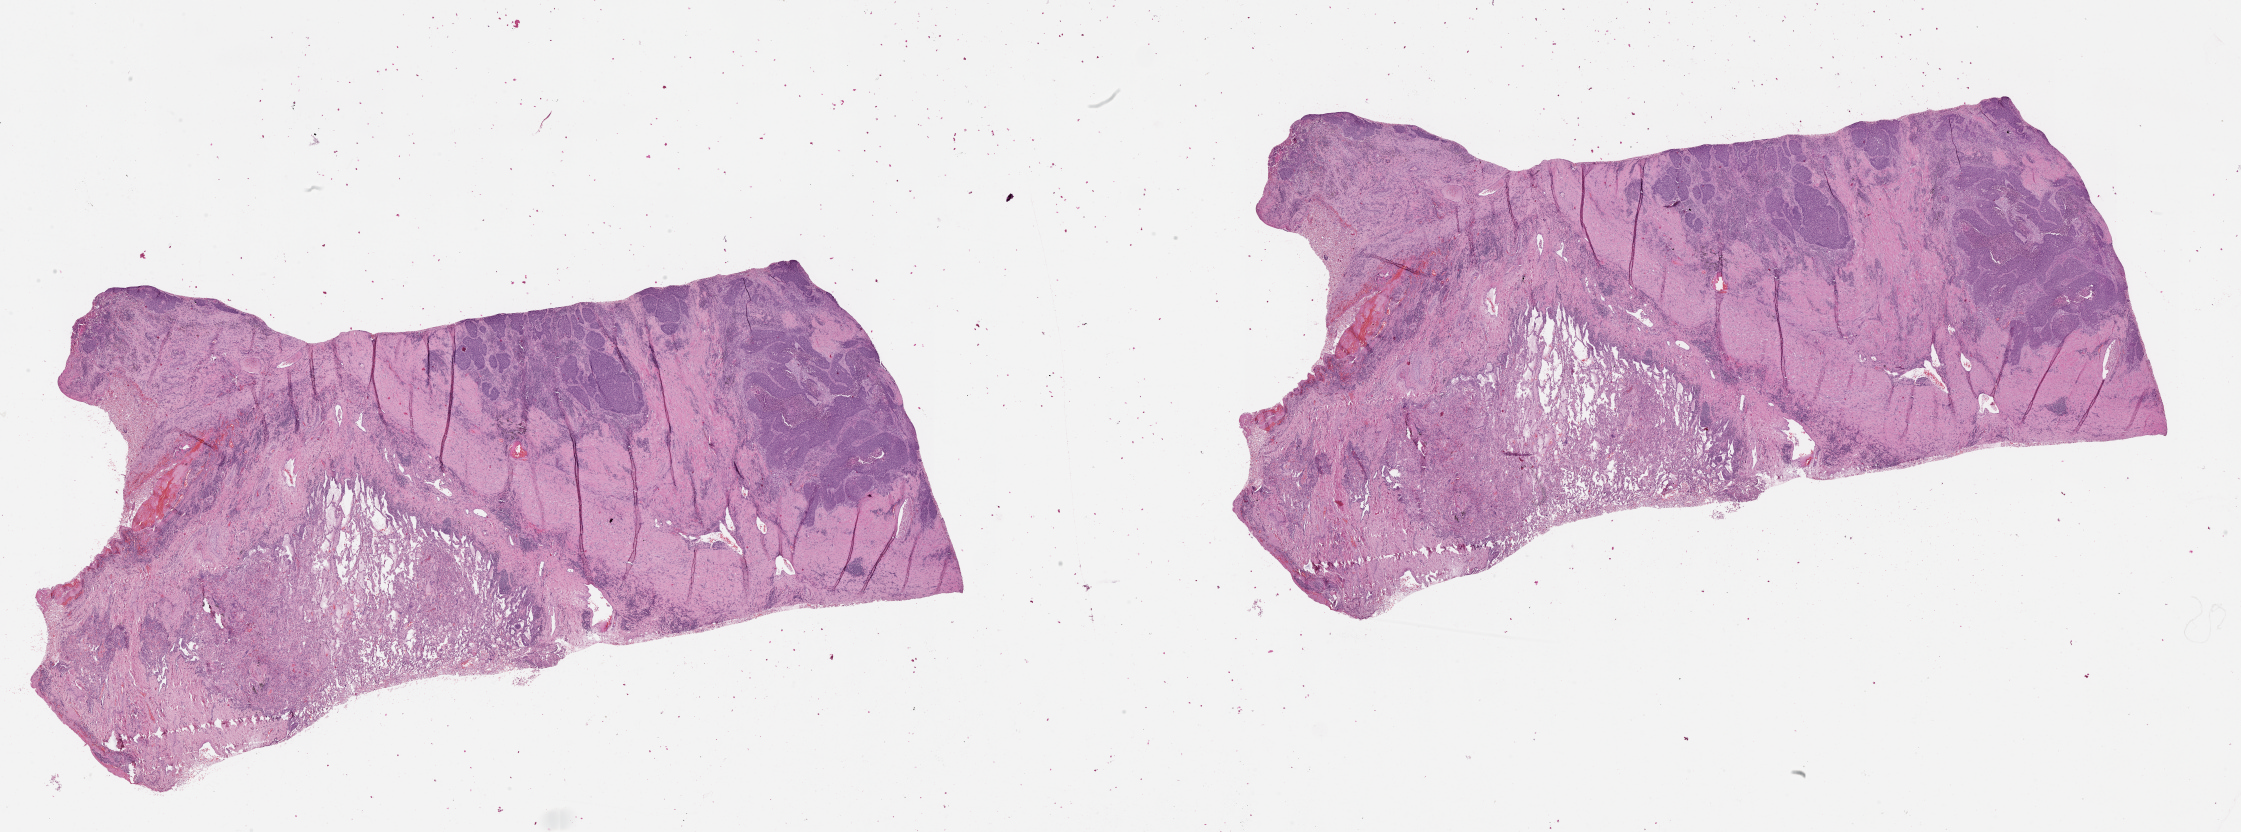
Digitized H&E tissue section (whole slide) — low-resolution overview of the scanned area, about 36.1 x 13.4 mm. Tumour tissue sample, lung. Patient: male, age 69 years.
Patient diagnosis (cohort enrolment): squamous cell carcinoma (lung).